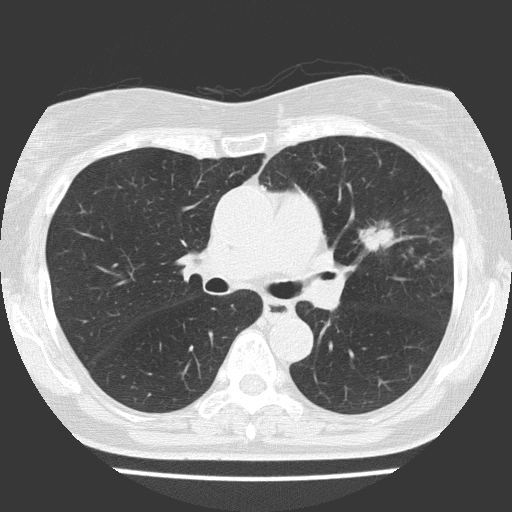
Low-dose screening chest CT, one axial slice; position 90 of 151 along the scan axis; reconstruction kernel FC51; 120 kVp; lung window (W 1500 / L -600 HU); 2 mm slice thickness; 512 × 512 image matrix, field of view 309 × 309 mm.
Structures marked on this image (manually delineated by an expert):
- lesion 1 (tumor, upper lobe of left lung): bounding box [x1, y1, x2, y2] px = [359, 222, 394, 251]